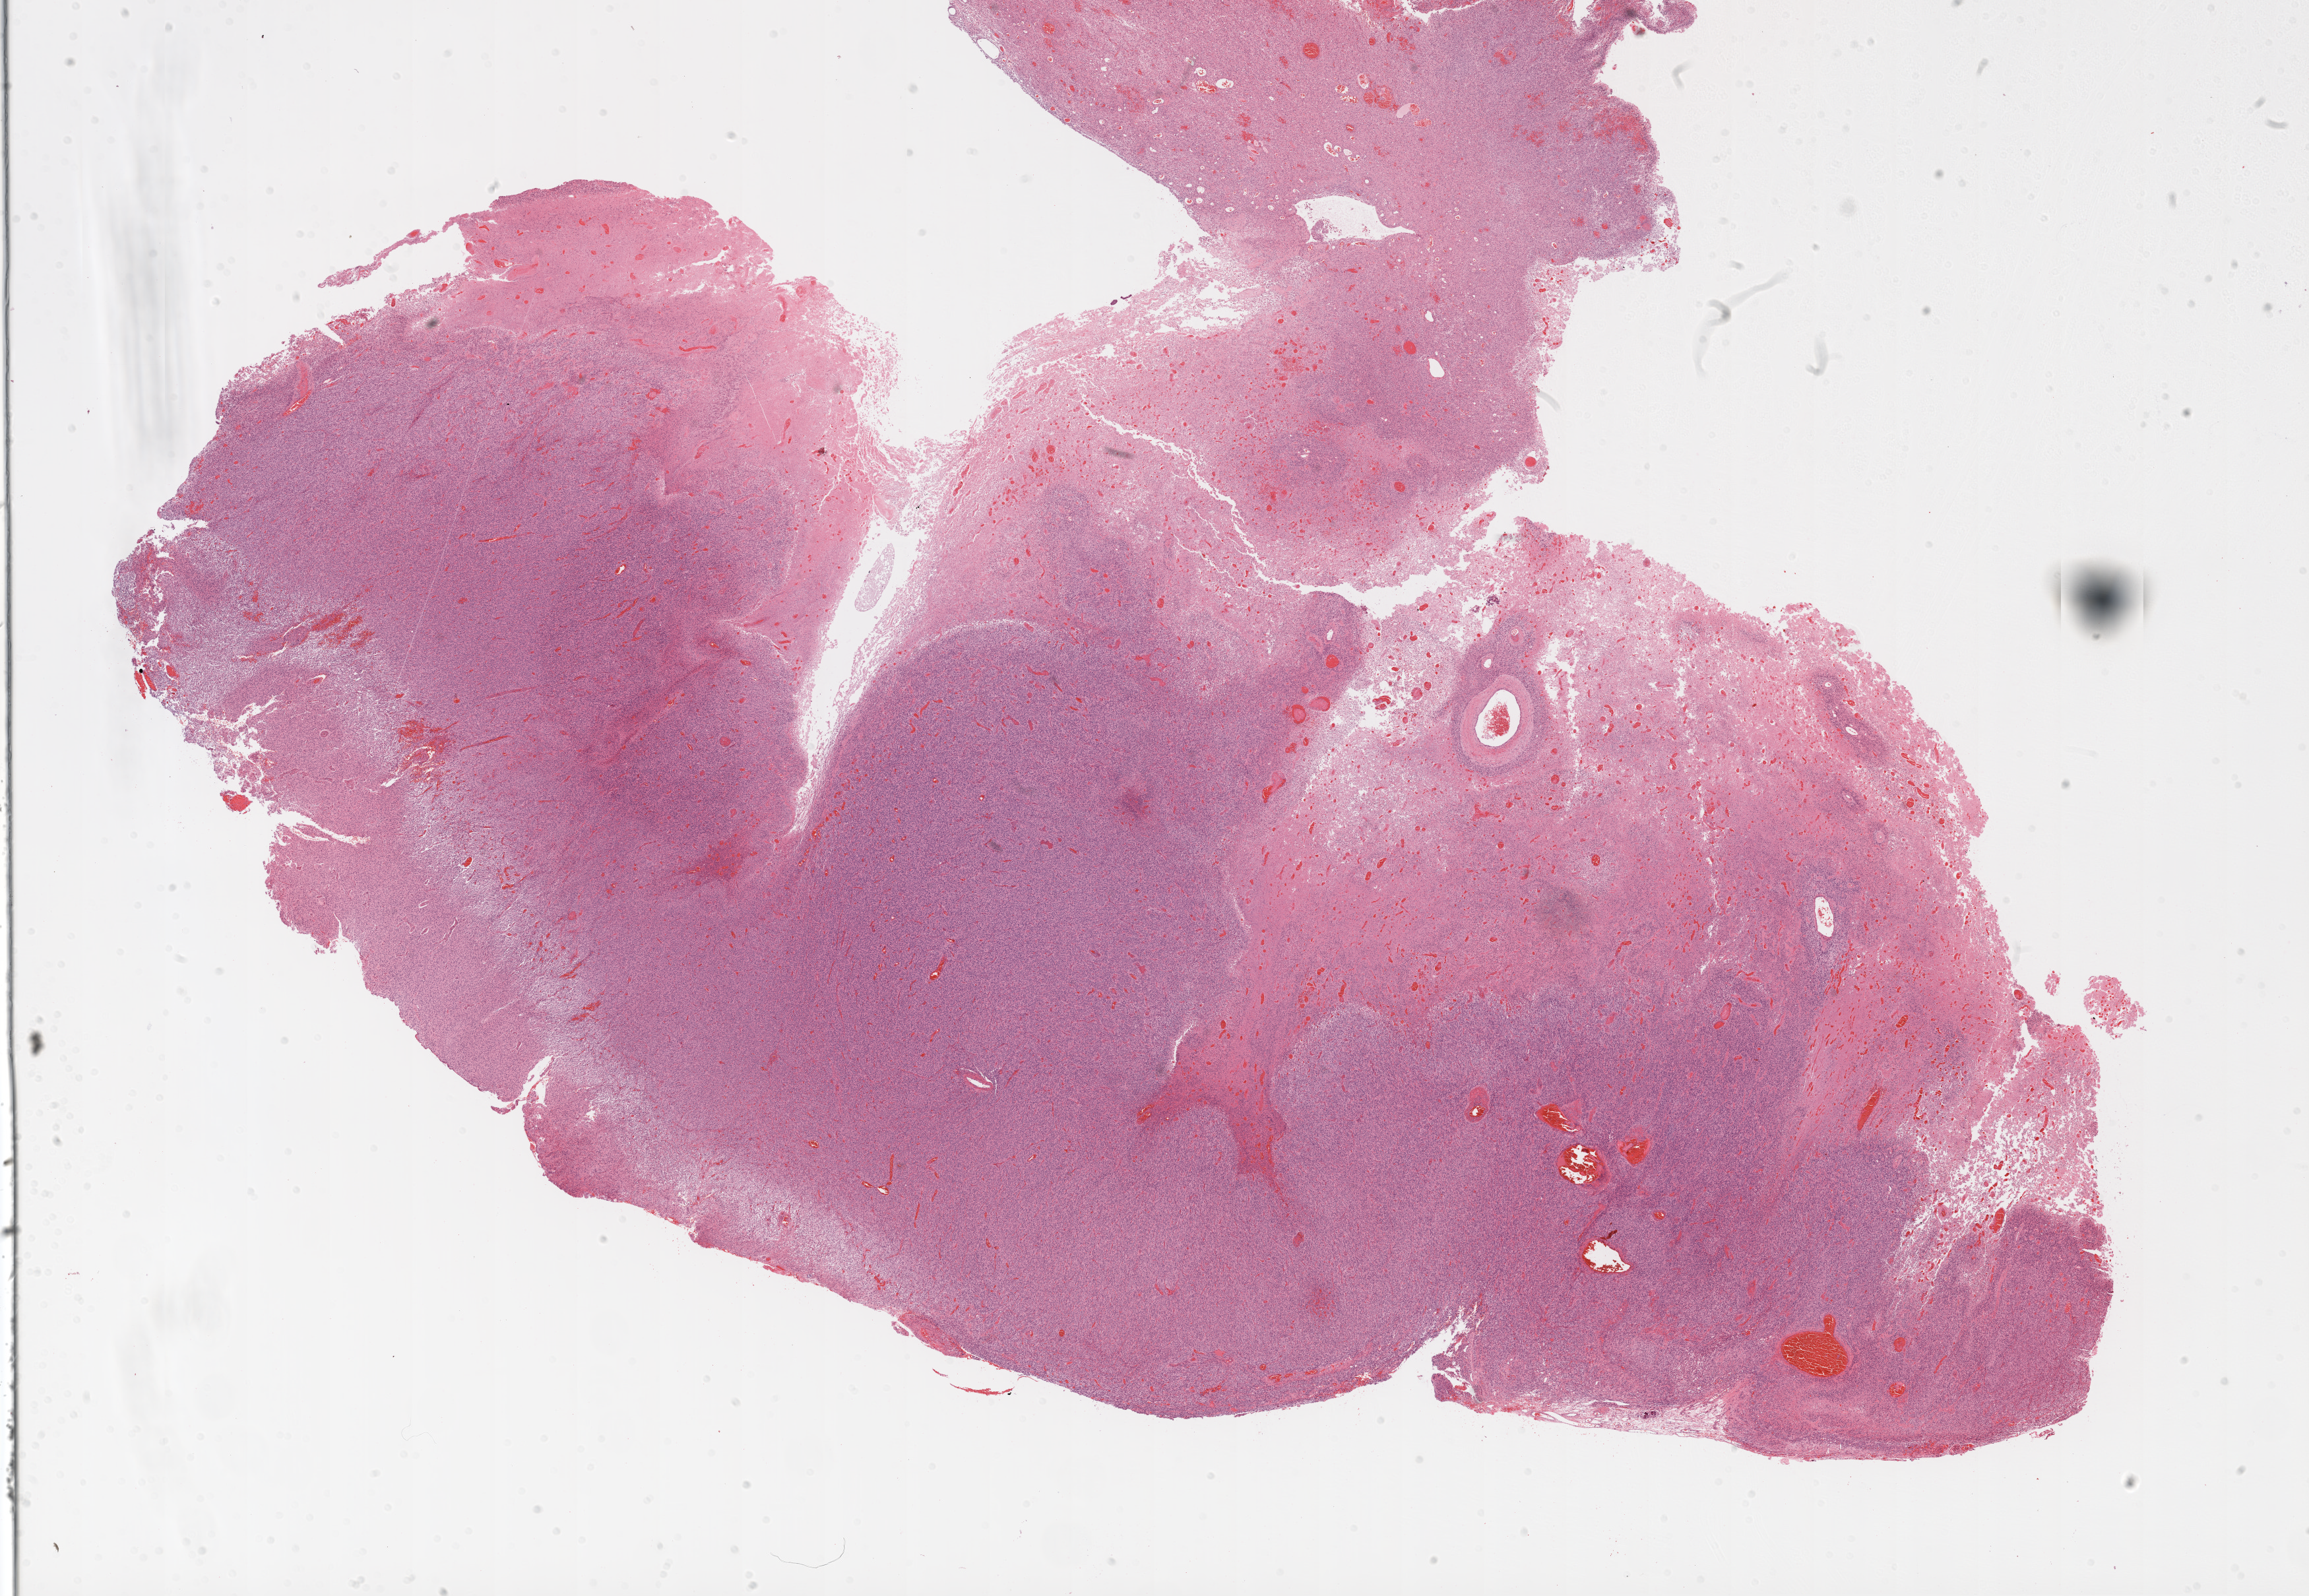
H&E whole-slide image — low-resolution overview of the scanned area, about 28.1 x 19.4 mm (acquisition: 20x scan). FFPE section. Brain, primary tumour sample. Female, age 63 years at initial diagnosis.
• histologic diagnosis: Glioblastoma